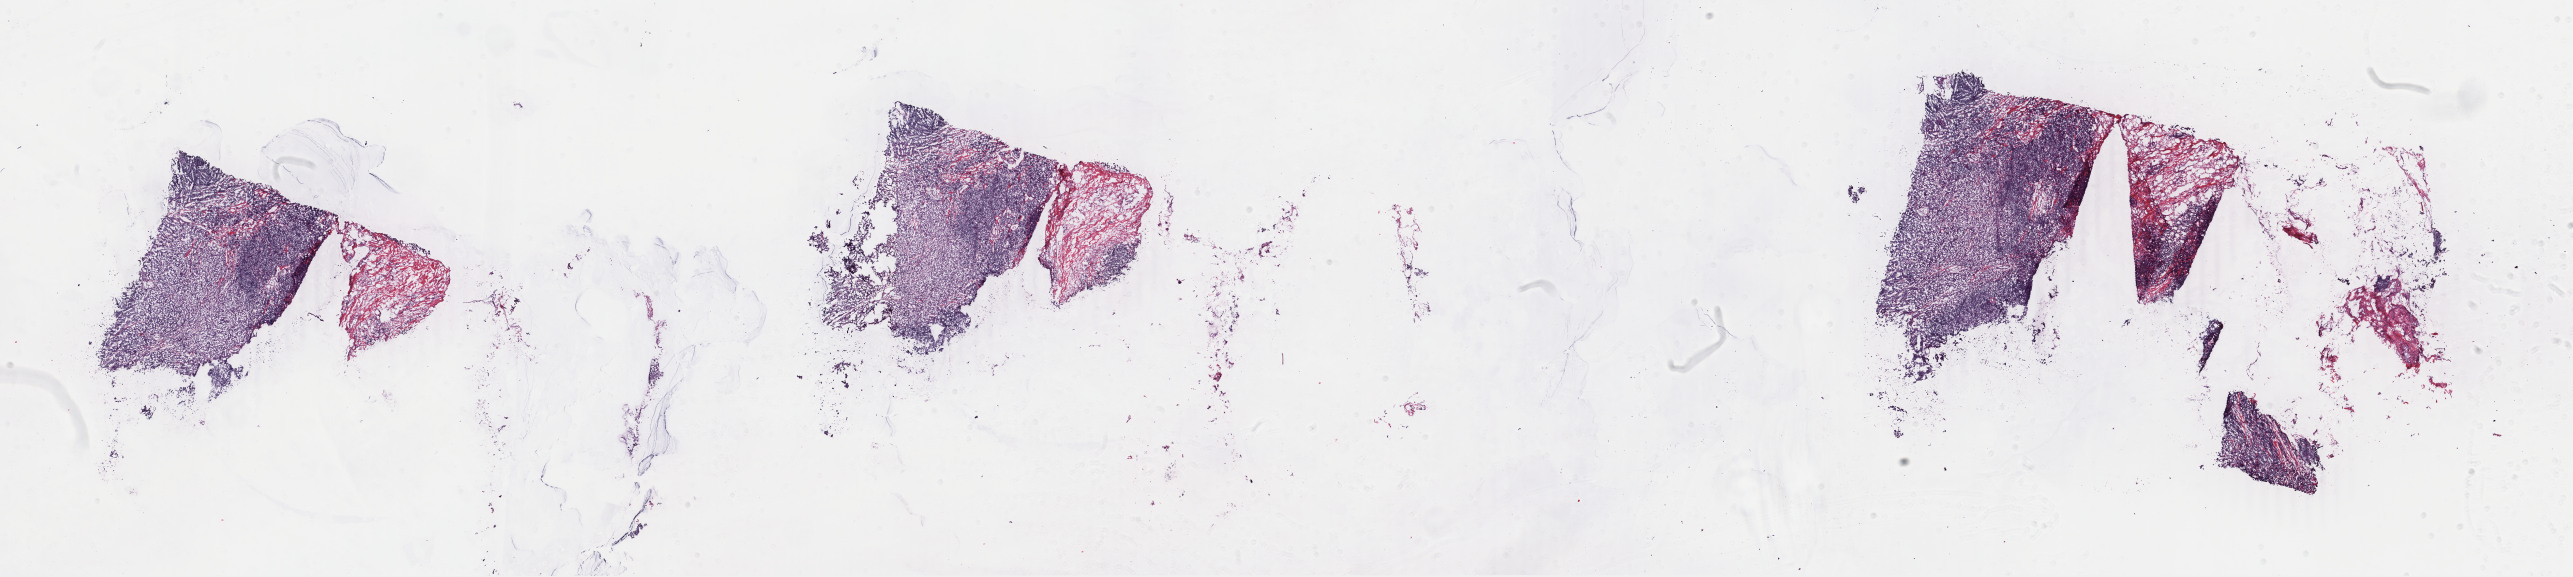
H&E-stained whole-slide image — a low-resolution overview of the entire scanned area, about 40.9 x 9.2 mm (from a 40x scan); frozen section; breast, primary tumour sample. Female, age 64 years at initial diagnosis. Composition of this section per pathologist review: tumour cells 90%, tumour nuclei 90%, normal cells 0%, stromal cells 10%, necrosis 0%. Inflammatory infiltration, as recorded: lymphocyte infiltration 1%, monocyte infiltration 0%, neutrophil infiltration 0%.
AJCC pathologic stage: IIA. Diagnosis: Infiltrating duct carcinoma, NOS. Laterality: right. Lymph nodes positive (case pathology): 0 of 12 examined.